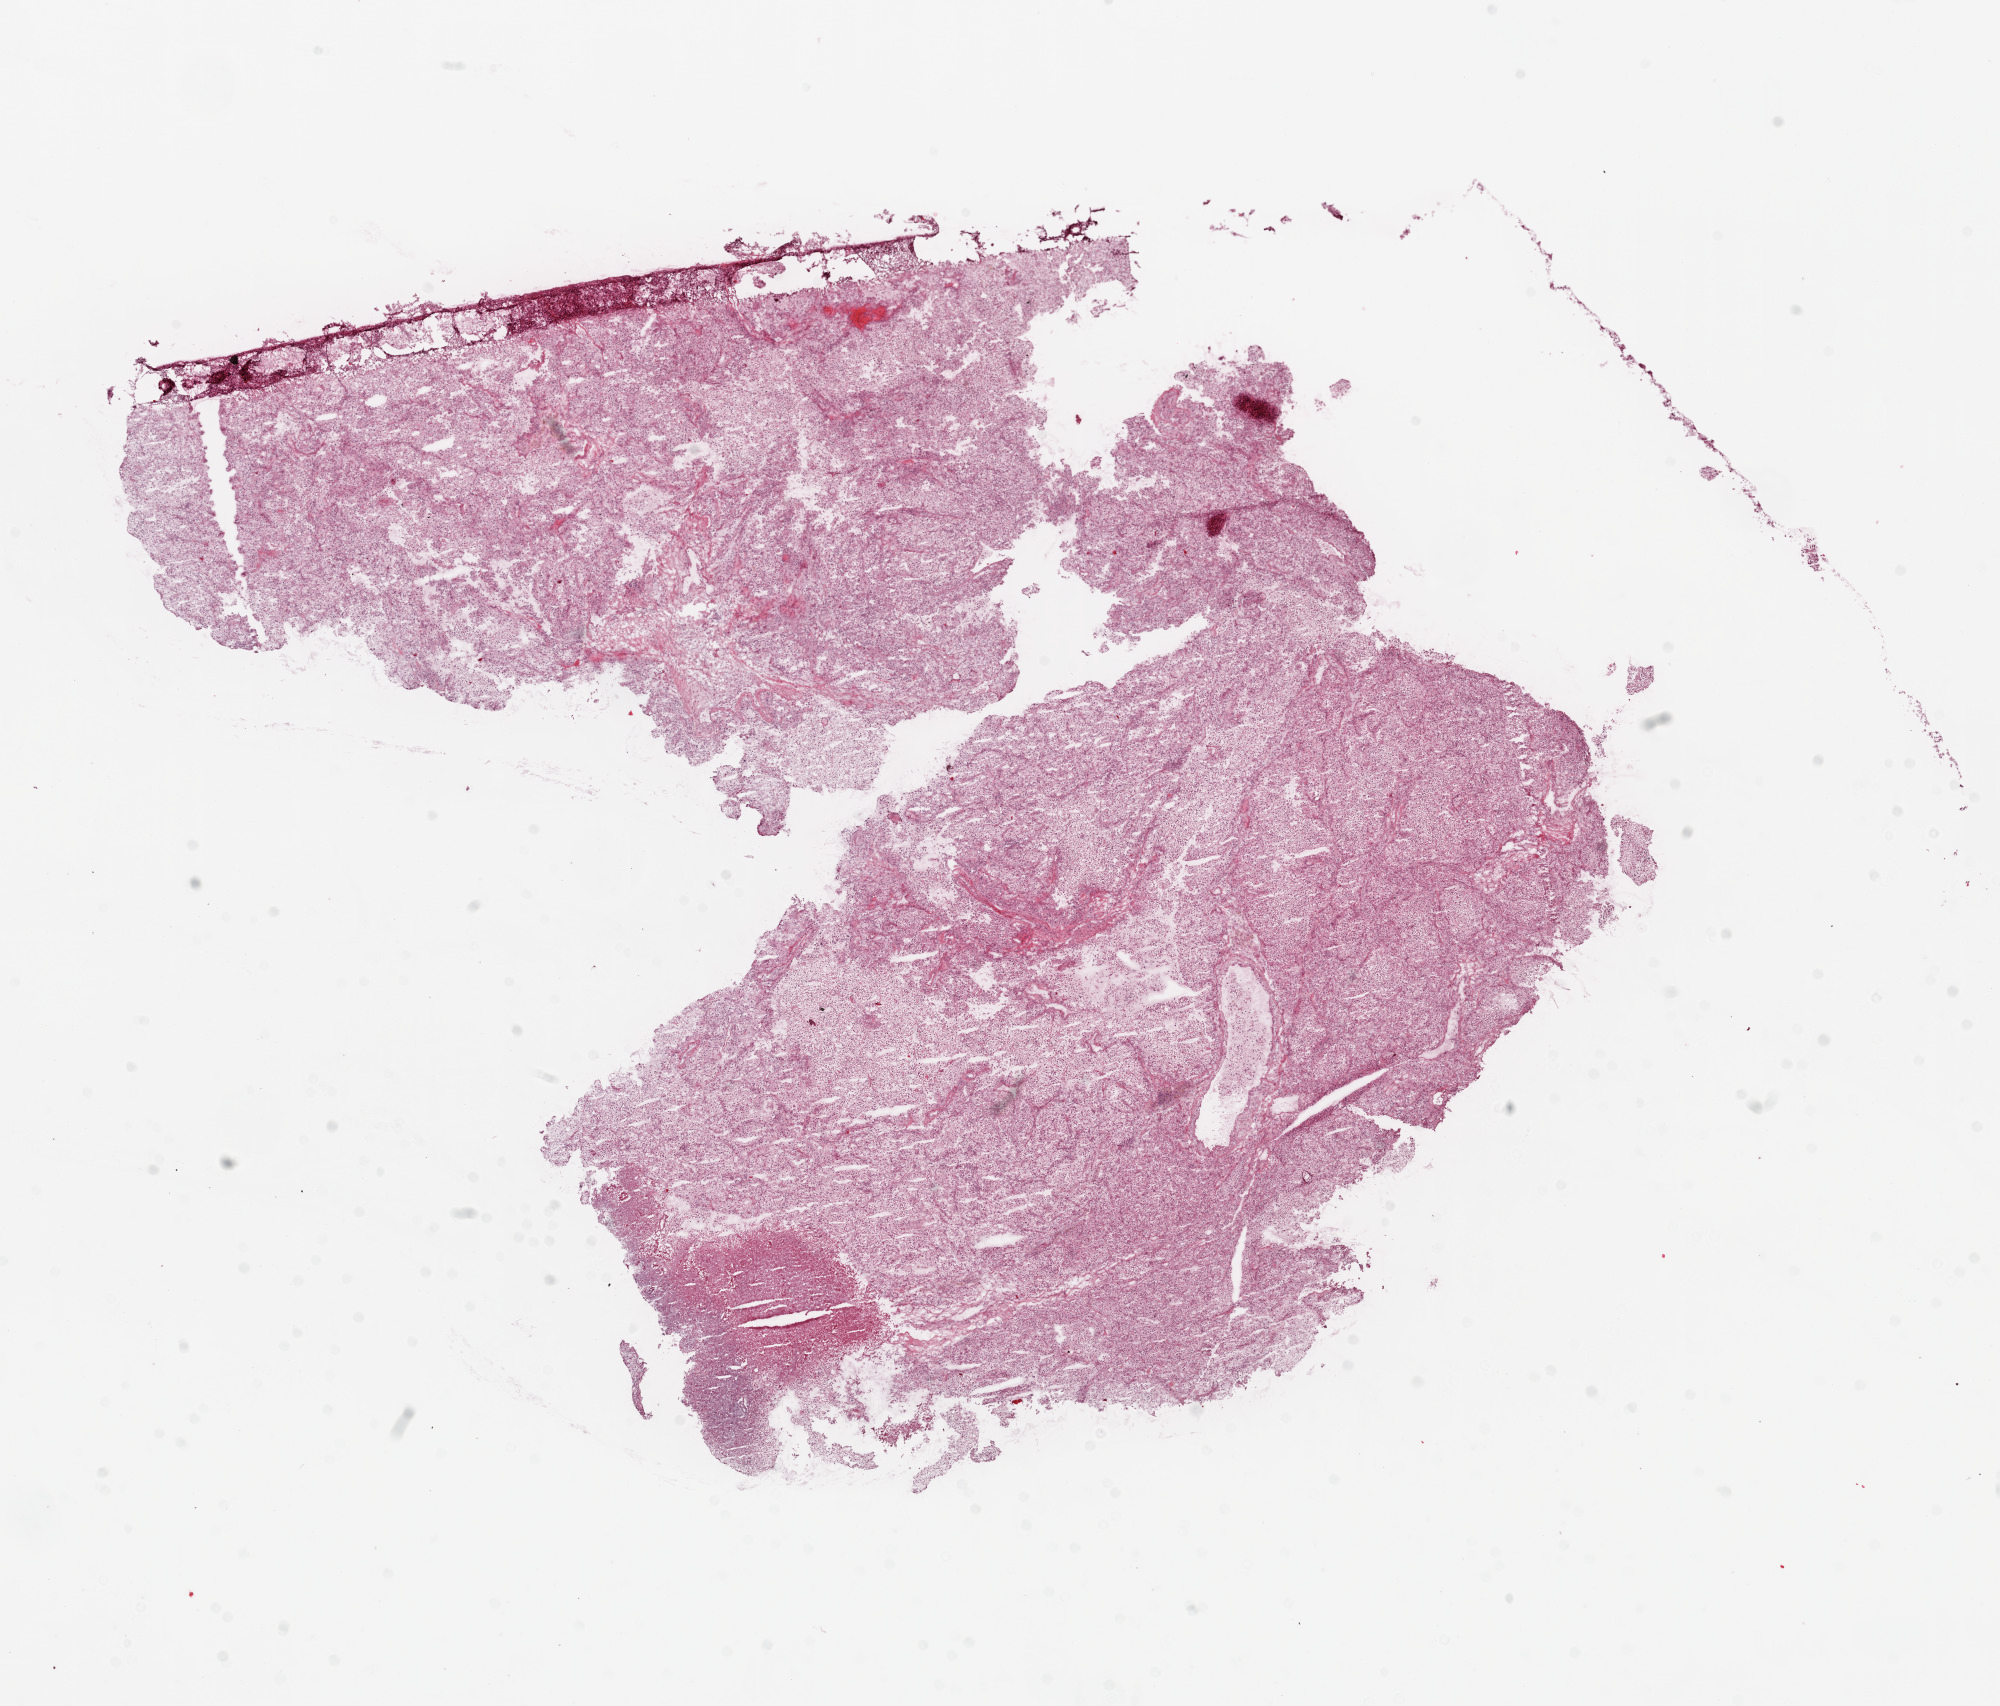
H&E whole-slide image, whole scanned area (about 16.0 x 13.7 mm, acquisition: 20x scan) shown as a low-resolution overview. Frozen section. Primary tumour sample from the kidney. Male, age 52 years at initial diagnosis. Histologic grade: G3 (poorly differentiated). Pathologist review of this section (percent, as recorded): tumour cells 90%, tumour nuclei 85%, normal cells 0%, stromal cells 10%, necrosis 0%.
AJCC pathologic stage: I. Pathologic diagnosis: Clear cell adenocarcinoma, NOS.